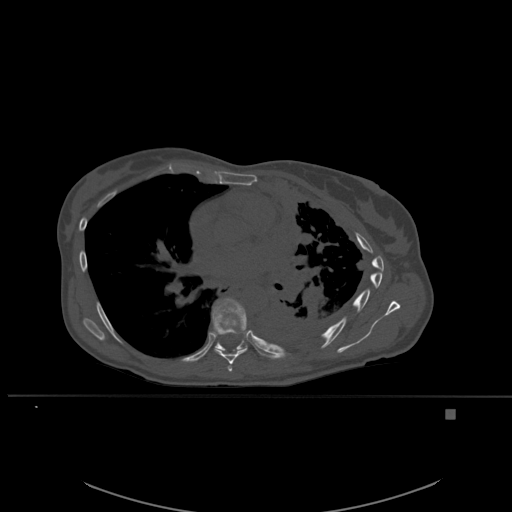
CT including the spine, one axial slice. Position 361 of 537 along the scan axis. Bone window (W 1800 / L 400 HU). 512 × 512 image matrix, field of view 440 × 440 mm. Female patient, age 45 years. From the clinical record (not read from this slice): primary cancer: lung.
Annotated regions visible in this slice (semi-automatically segmented with operator editing):
- T6 vertebra: bounding box [x1, y1, x2, y2] px = [227, 363, 233, 372]
- T7 vertebra: [212, 298, 248, 364]
- T8 vertebra: [212, 298, 247, 353]